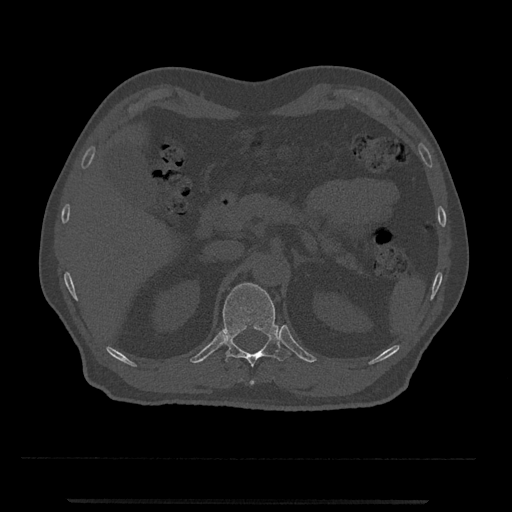
CT including the spine, one axial slice. Slice 403 of 797 in the series (ordered by position). 120 kVp. Bone window (W 1800 / L 400 HU). 0.5 mm slice thickness. 512 × 512 image matrix, field of view 419 × 419 mm. Patient: male, 63 years. From the clinical record (not read from this slice): primary cancer: prostate.
Annotated regions visible in this slice (semi-automatic segmentation, software-assisted and operator-edited):
- T12 vertebra: bounding box (x1, y1, x2, y2) in pixels: (221, 282, 290, 385)